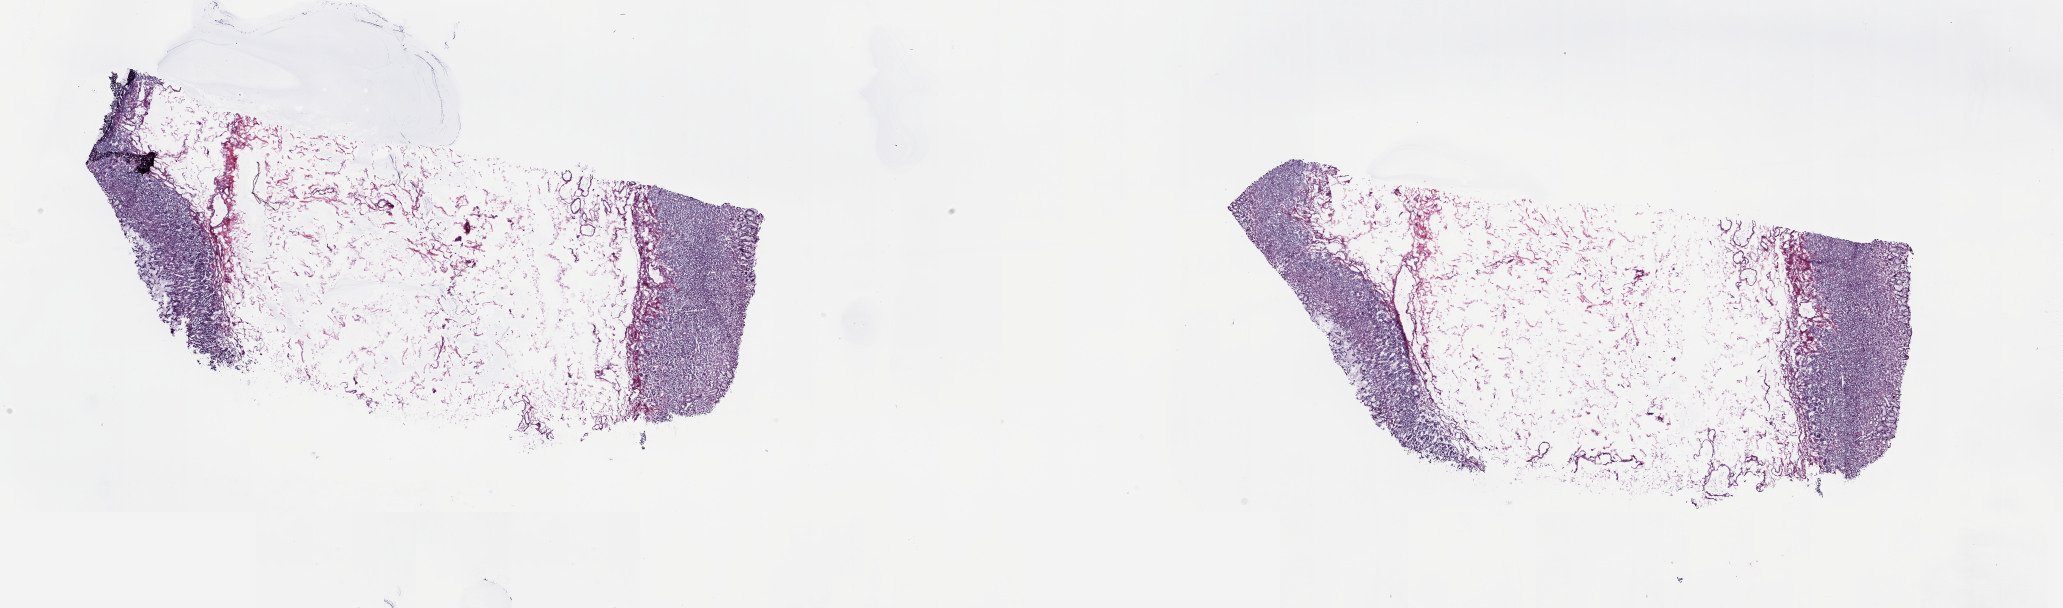
Whole-slide histology image, H&E — shown as a low-resolution overview of the whole scanned area (about 32.7 x 9.6 mm, acquisition: 20x scan), frozen section from the top of the tissue portion, sample: solid tissue normal (non-tumour tissue), esophagus. Patient: male, age at initial diagnosis 80 years. Slide review estimates, as recorded: tumour cells 0%, tumour nuclei 0%, normal cells 100%, stromal cells 0%, necrosis 0%. Infiltration values recorded for this section: lymphocyte infiltration 3%, monocyte infiltration 0%, neutrophil infiltration 0%.
This section: solid tissue normal (non-tumour) sample from the same patient. Patient diagnosis: Adenocarcinoma, NOS (lower third of esophagus).